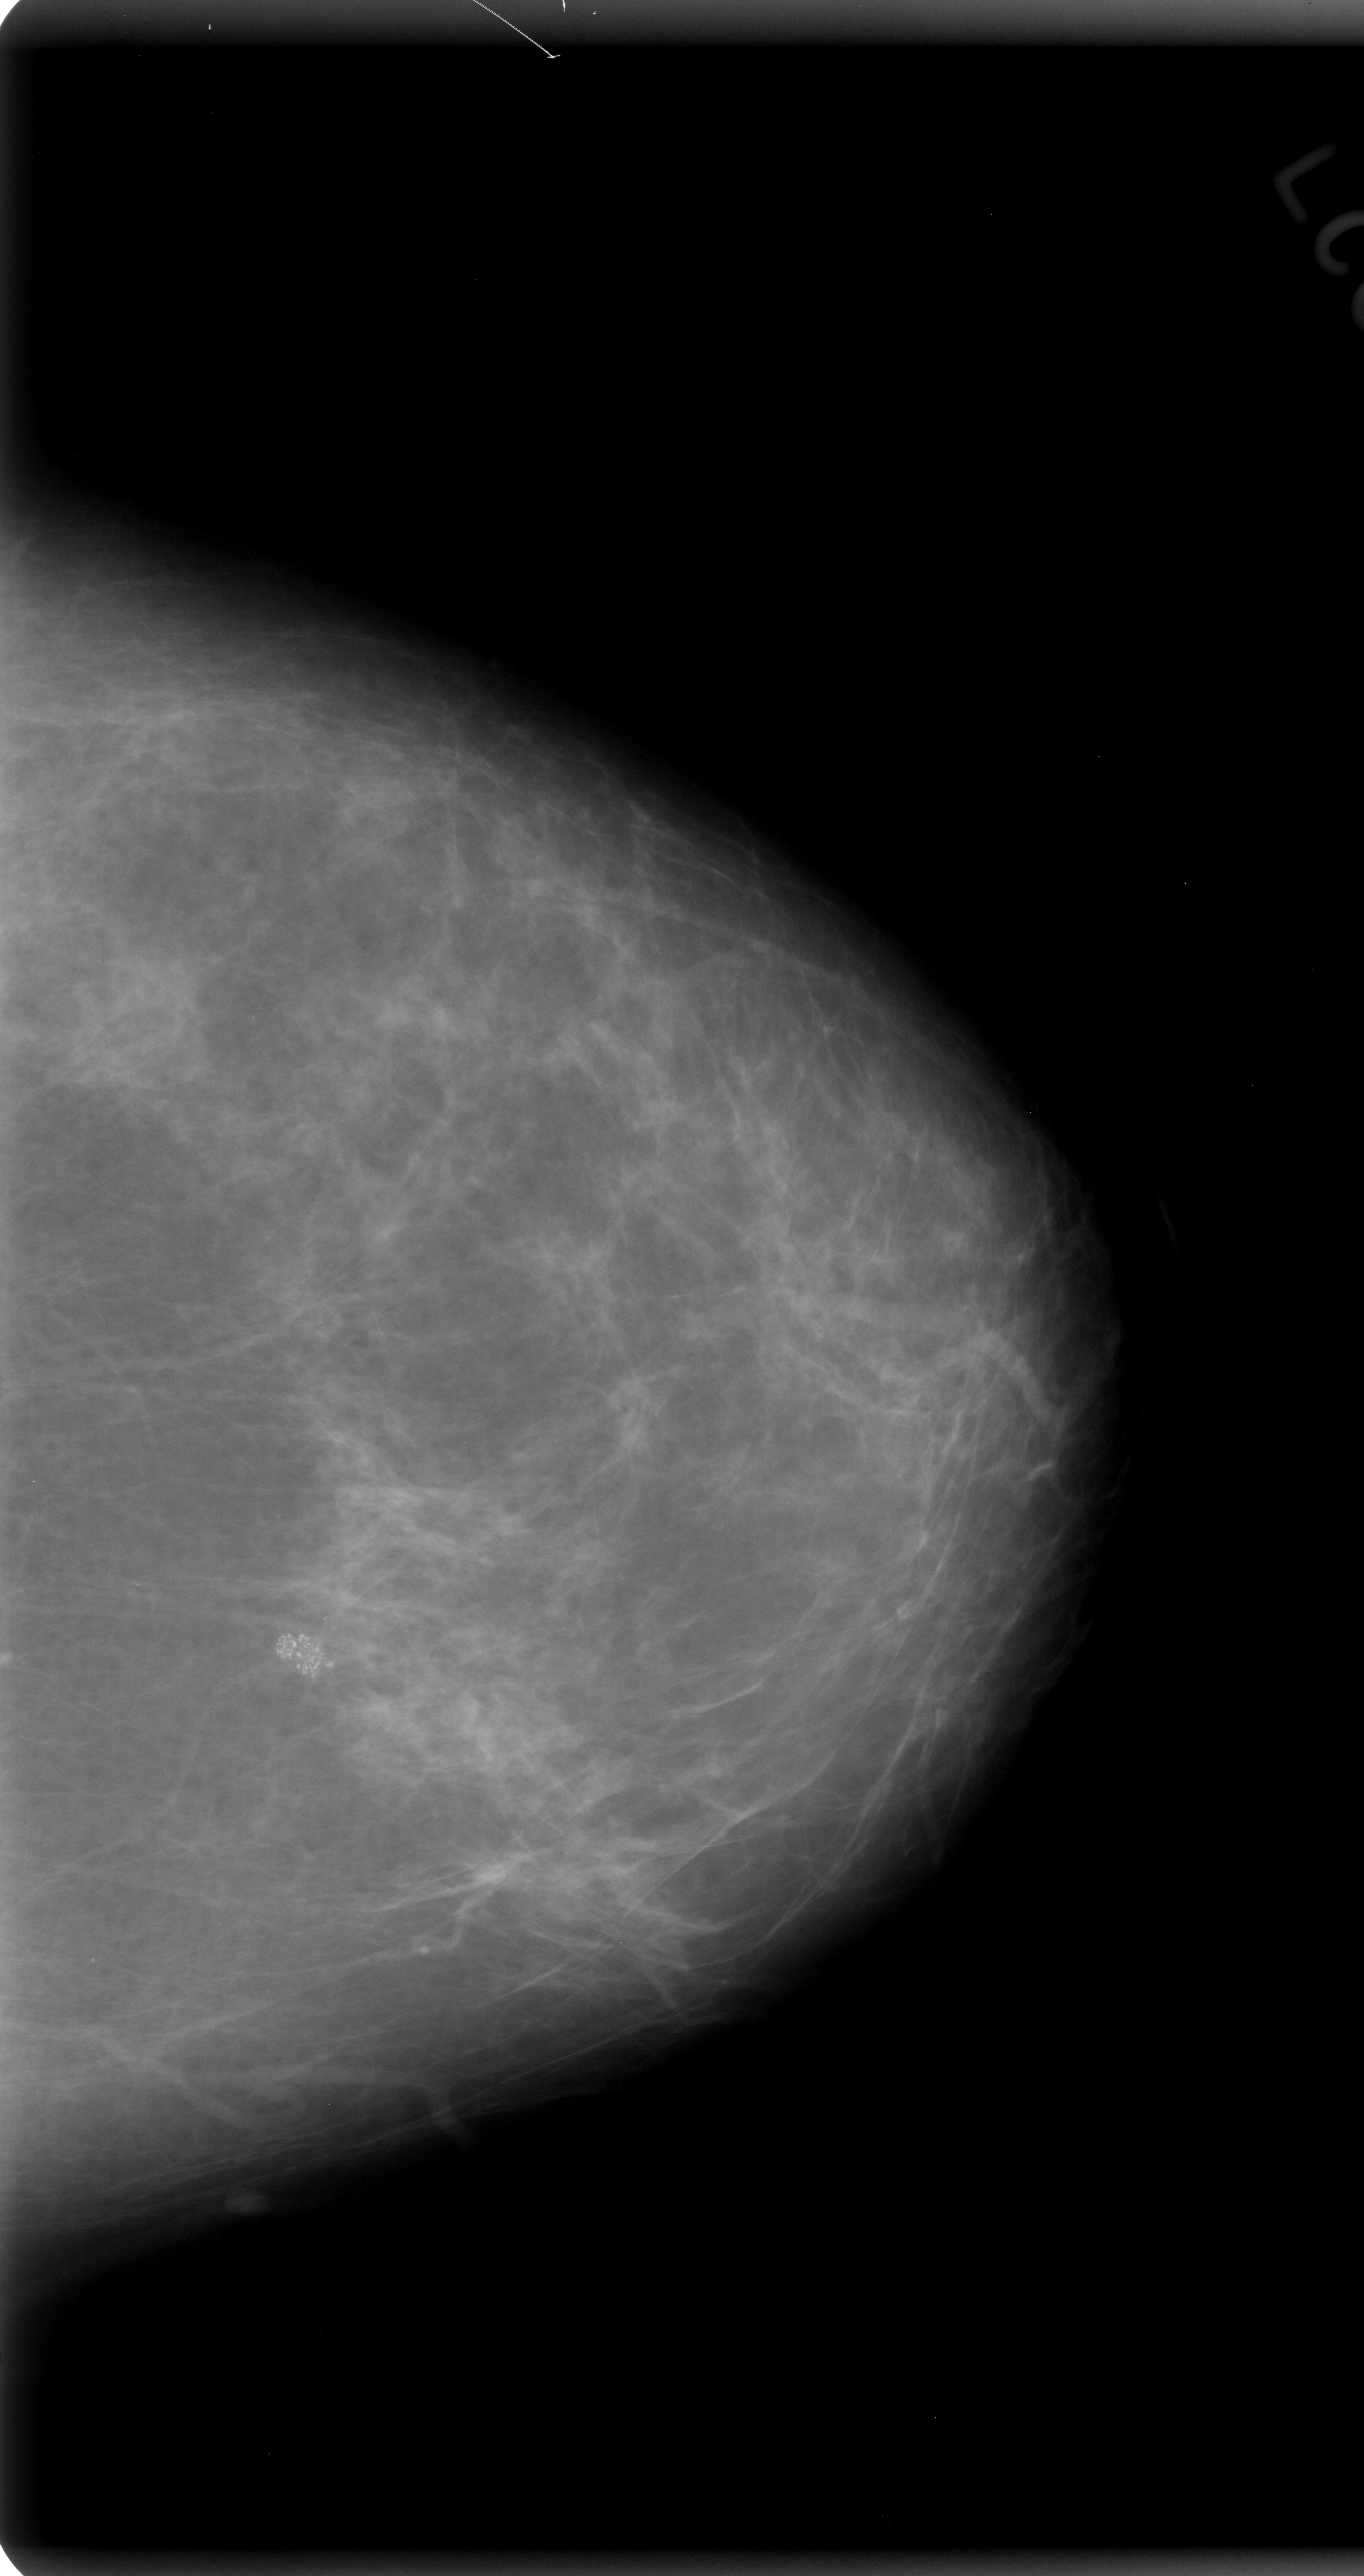
Scanned film-screen mammogram; left breast; craniocaudal (CC) view; BI-RADS breast density category 2 (scale 1–4).
Calcifications, morphology pleomorphic, distribution clustered; BI-RADS assessment category 5; subtlety rating 5 on a 1 (subtle) to 5 (obvious) scale; pathology result (as recorded, not read from the image): malignant.